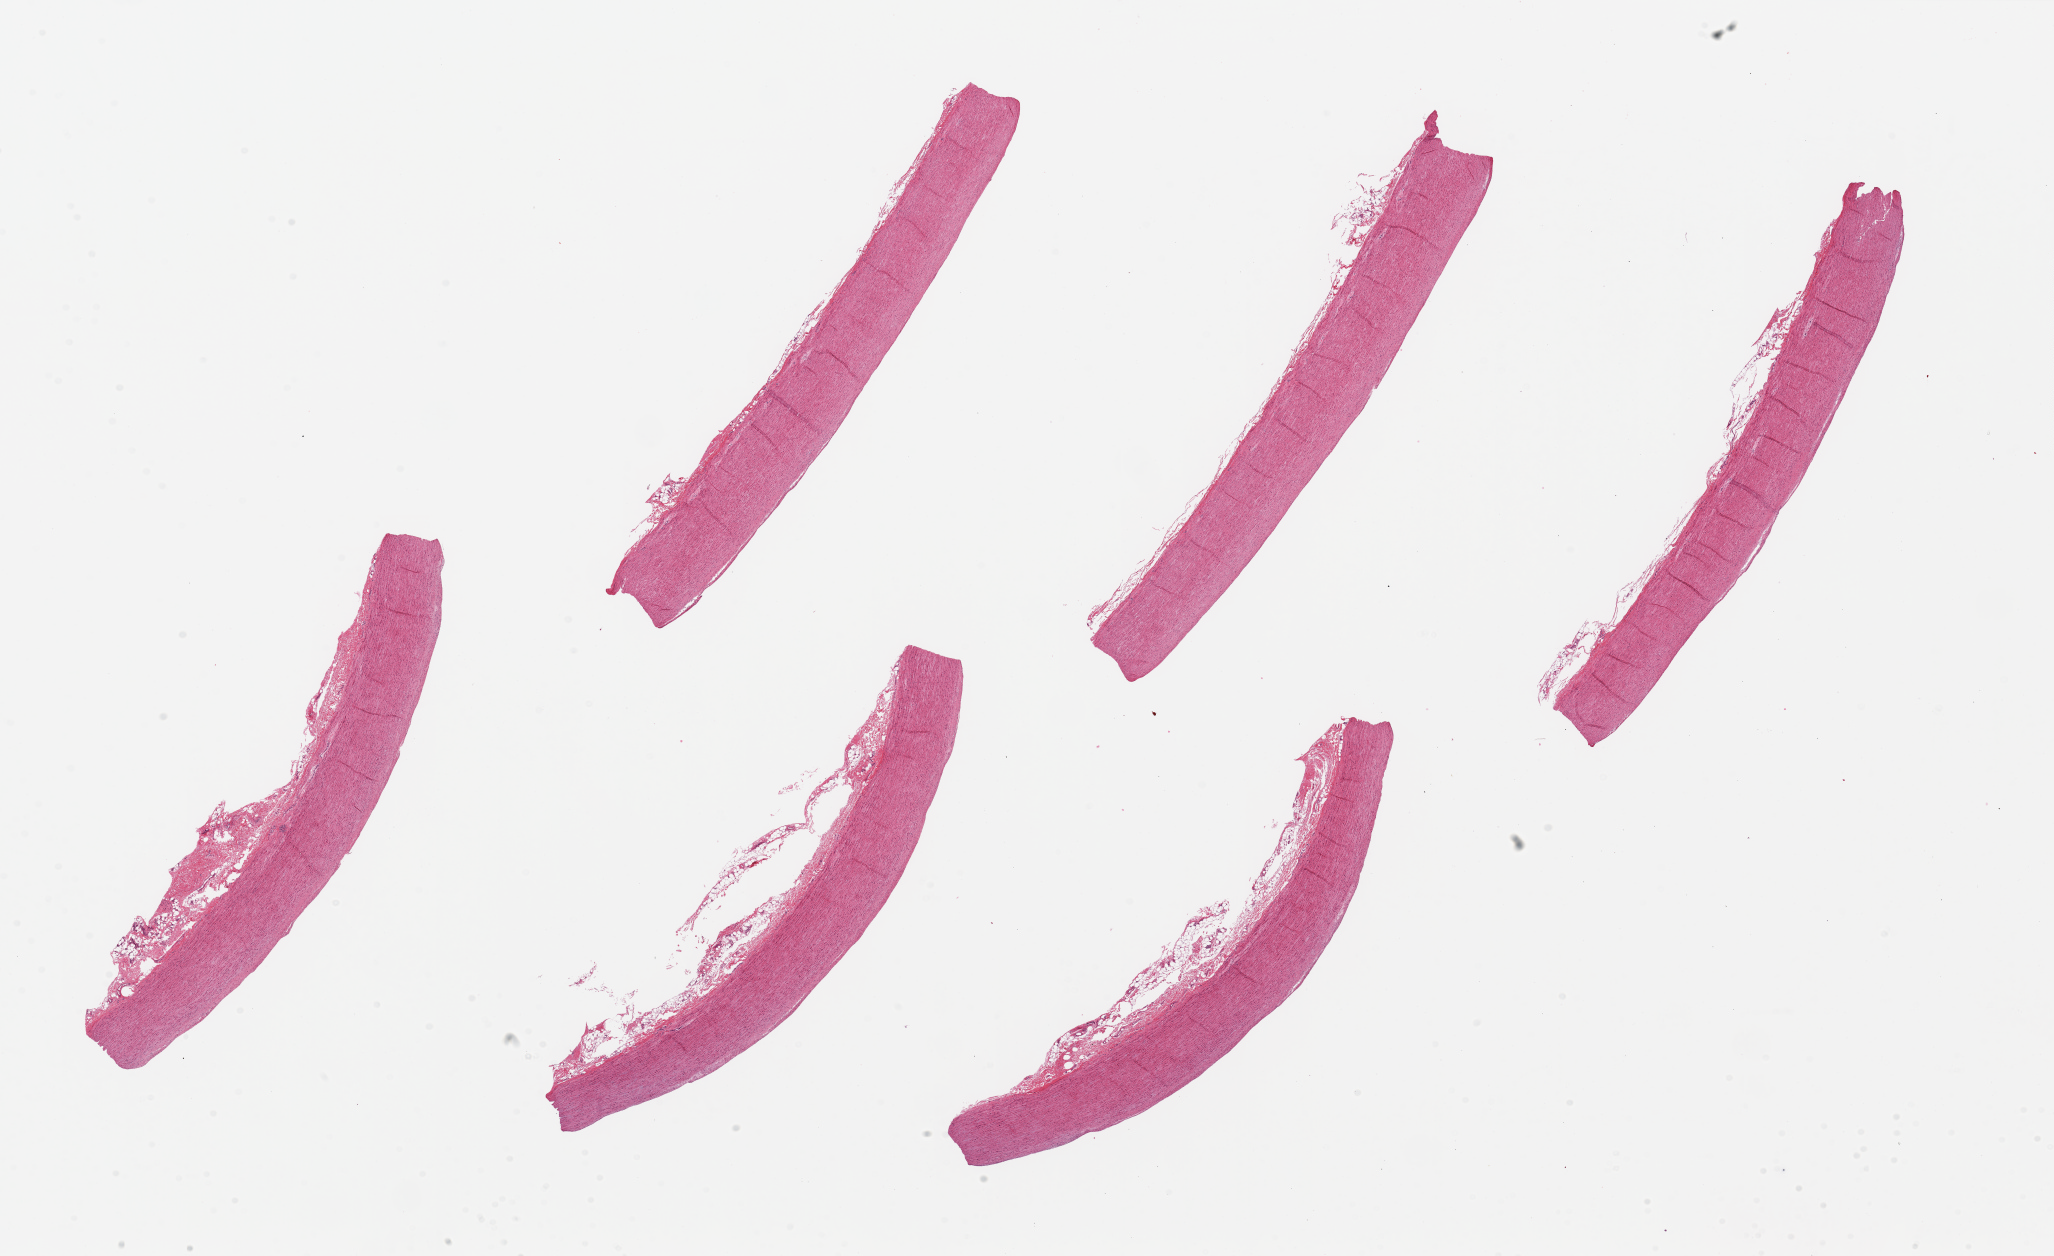
Whole-slide image, haematoxylin and eosin stain, brightfield — shown as a low-resolution overview of the whole scanned area (about 32.5 x 19.9 mm), PAXgene-fixed, paraffin-embedded tissue, sampled site (target tissue): aorta, tissue donor sample. Donor: male.
Pathologist's review note for this sample: 6 pieces, up to 10x2mm; small amount of untrimmed adventitial stroma.